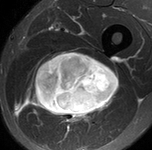
MRI of an extremity soft-tissue mass, one axial slice. Position 69 of 90 along the scan axis. STIR. MR volume resampled by the dataset authors to the PET/CT grid (not the native acquisition matrix). 3.27 mm slice thickness. 152 × 150 image matrix, field of view 148 × 146 mm. Male patient. Case-level facts recorded for this patient, not image findings: histological type: undifferentiated pleomorphic liposarcoma; grade: high; site of the primary tumour: left thigh.
Outlined on this slice (expert contour drawn on MRI and transferred to this co-registered scan by the dataset authors):
- gross tumour volume including surrounding oedema: box from (x=22, y=51) to (x=119, y=127) px
- gross tumour volume (mass): (x=30, y=51)–(x=119, y=117)